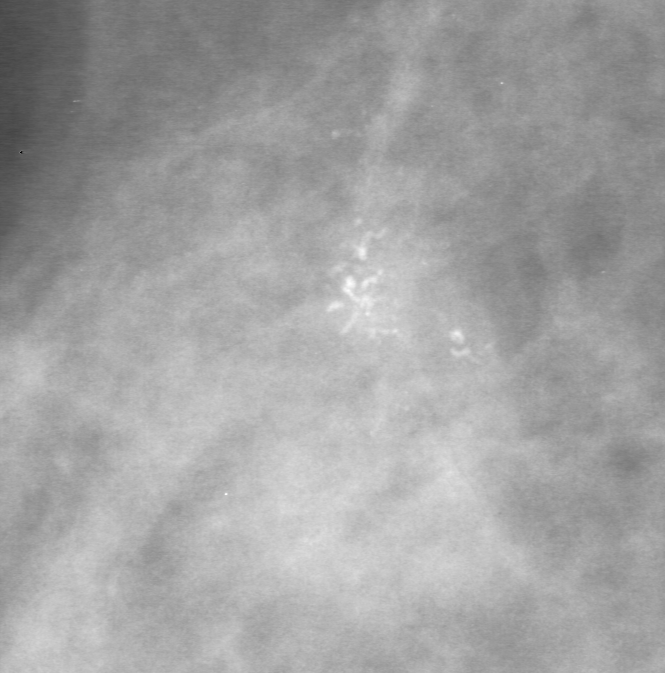
Cropped region of a digitized screen-film mammogram centred on a radiologist-marked abnormality, right breast, MLO view.
Calcifications, morphology fine linear branching, distribution clustered; BI-RADS assessment category 3; subtlety rating 5 on a 1 (subtle) to 5 (obvious) scale; pathology result (as recorded, not read from the image): malignant.